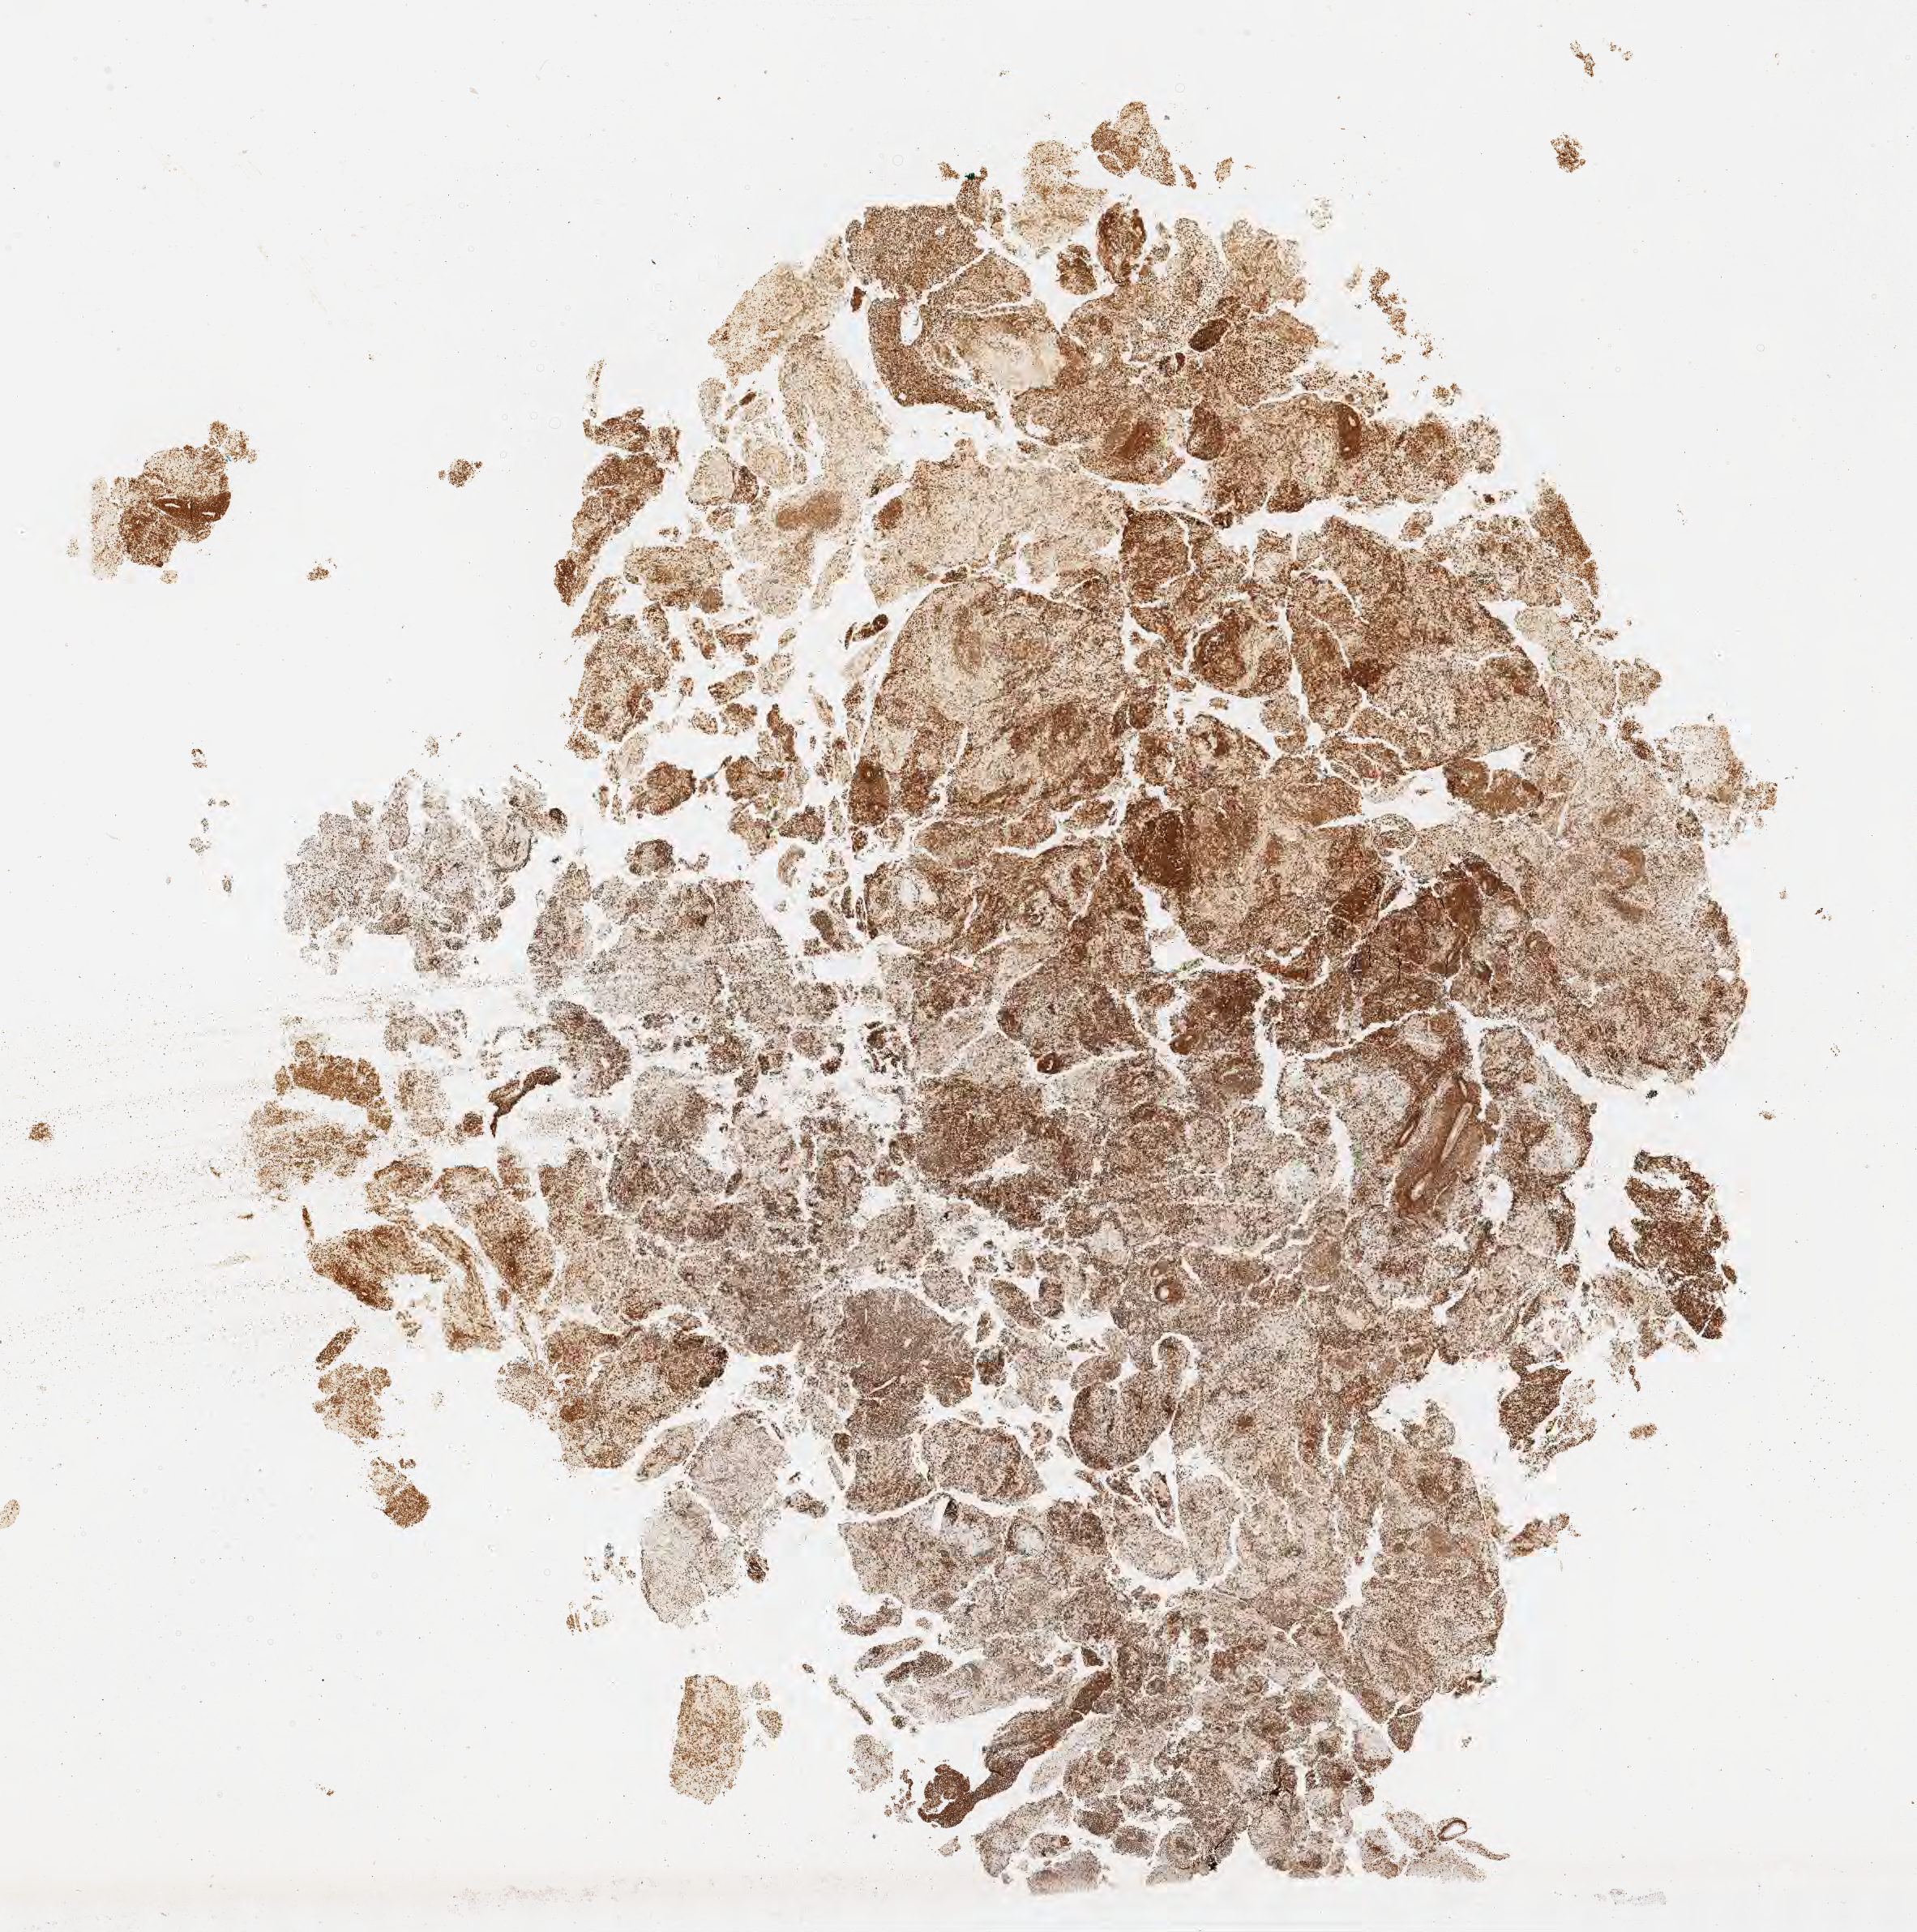
IHC for BCL2, whole-slide image — a low-resolution overview of the entire scanned area, about 19.1 x 19.3 mm. Specimen: tumor tissue. Anatomic site: brain. Patient male; aged 51.
• histologic diagnosis: Diffuse large B-cell lymphoma, NOS